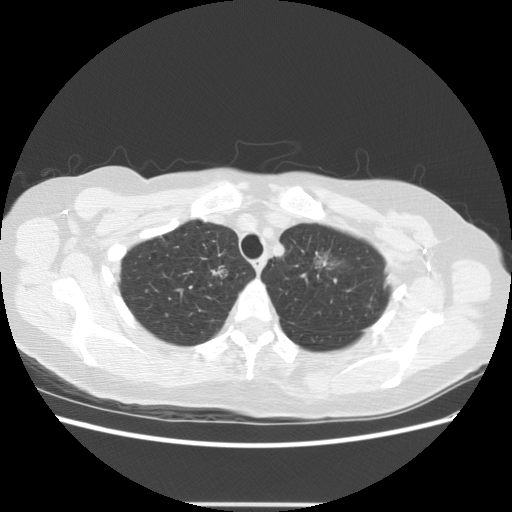
Axial slice from a low-dose chest CT screening exam, third annual screen, lung window (W 1500 / L -600 HU), standard (soft-tissue) reconstruction kernel (STANDARD), slice 105 of 126 in the series. Female participant, aged 65 years at enrolment. Former smoker at enrolment.
- Expert-annotated lung lesion, box from (x=291, y=231) to (x=366, y=294) px.
- Screening reader's record for this exam (one nodule recorded; not confirmed to be the boxed lesion): non-calcified nodule or mass ≥4 mm, left upper lobe, 17 × 14 mm, poorly defined margins, ground glass attenuation, pre-existing on the prior screen: yes; interval growth: yes.
- Official screen result: positive, other.
- Lung cancer was diagnosed 96 days after this screen: adenocarcinoma, NOS, left upper lobe, moderately differentiated (G2), stage IA (AJCC 6th edition), 30 mm at pathology.